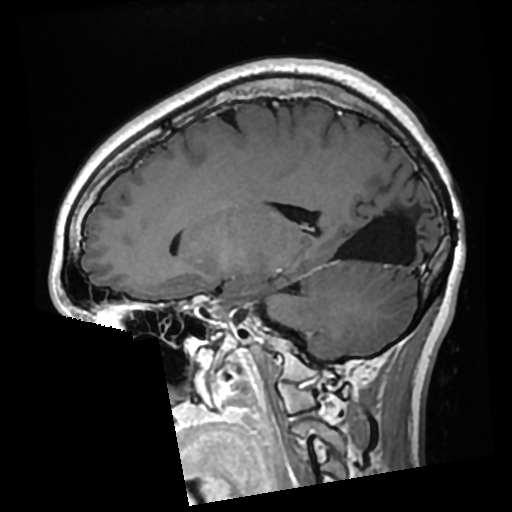
Brain MRI from a brain-tumour surgery series, one sagittal slice; slice 115 of 276 in the series (ordered by position); T1-weighted post-contrast; 0.7 mm slice thickness; 512 × 512 image matrix. From the clinical record (not read from this slice): histopathology: Glioma with ependymal features; WHO grade: 2; tumour location: Left Parietal.
Annotated regions visible in this slice (expert manual segmentation):
- previous resection cavity: bounding box [x1, y1, x2, y2] px = [338, 196, 420, 262]